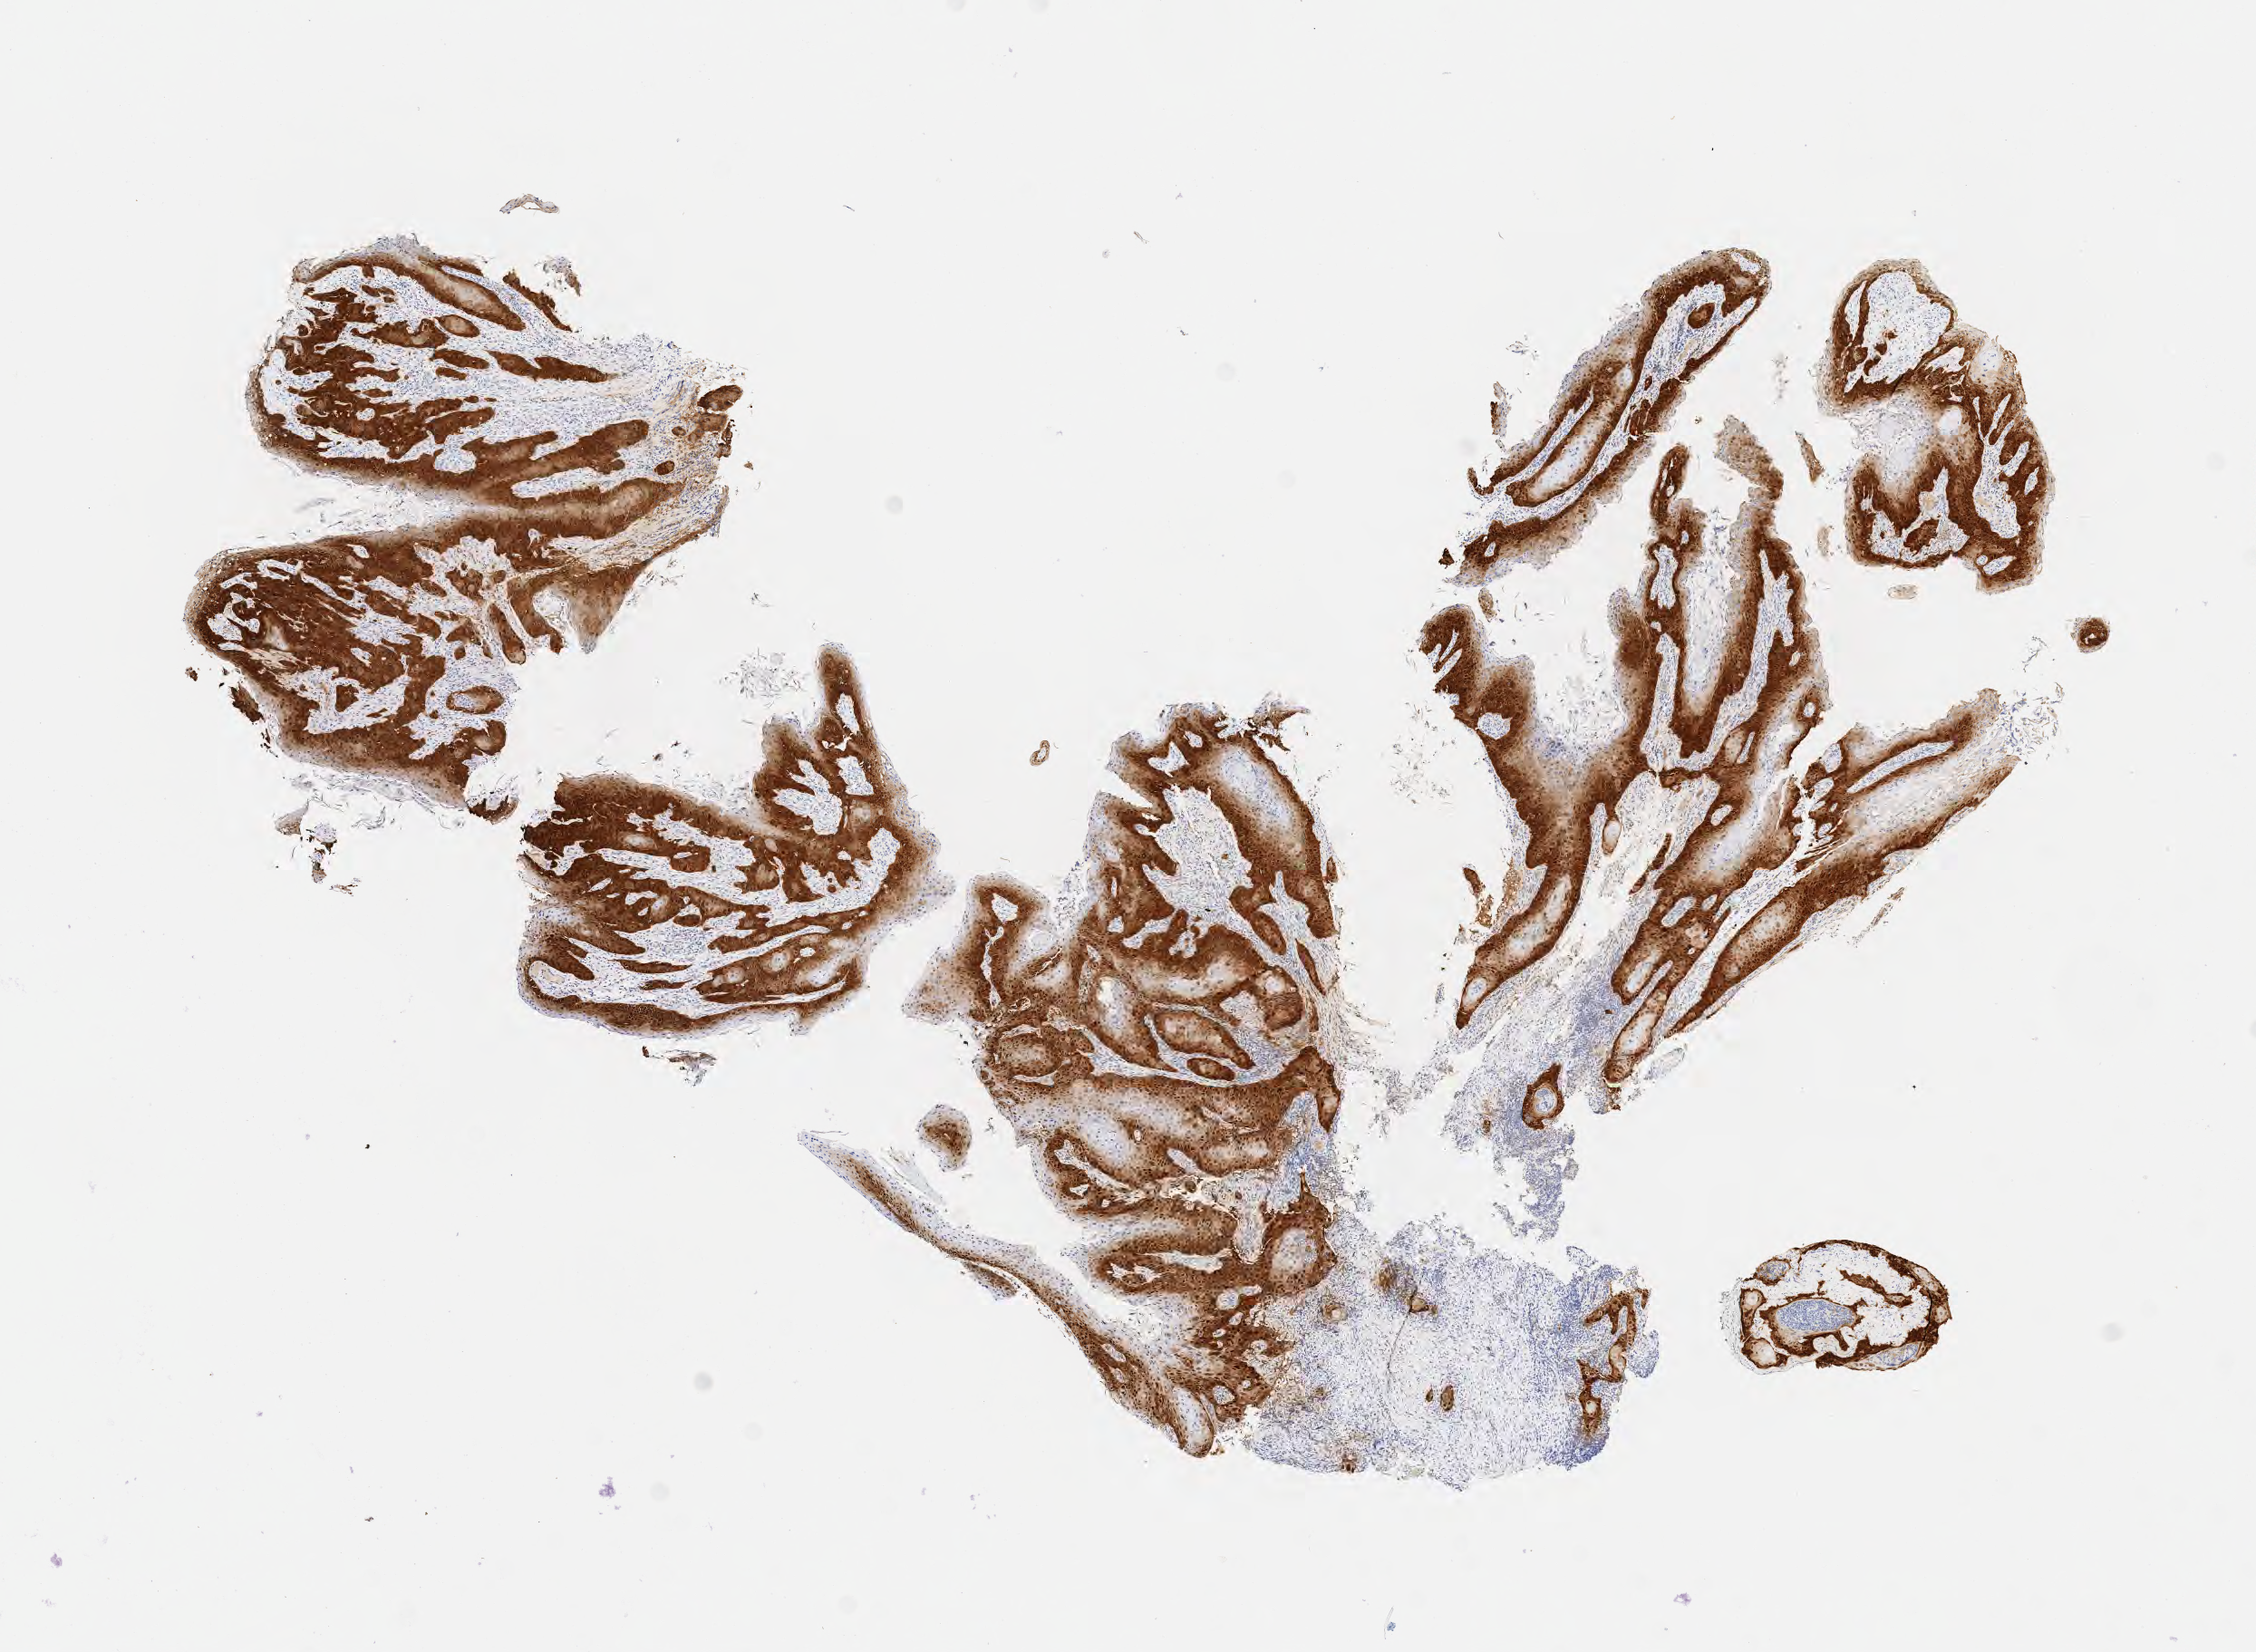
Immunohistochemistry (IHC) whole-slide image stained for p16 (p16INK4a), low-resolution overview of the scanned area, about 10.1 x 7.4 mm, tumor tissue, anatomic site: cervix. Patient: female, 68 years old.
Histologic diagnosis: Squamous cell carcinoma, keratinizing, NOS.